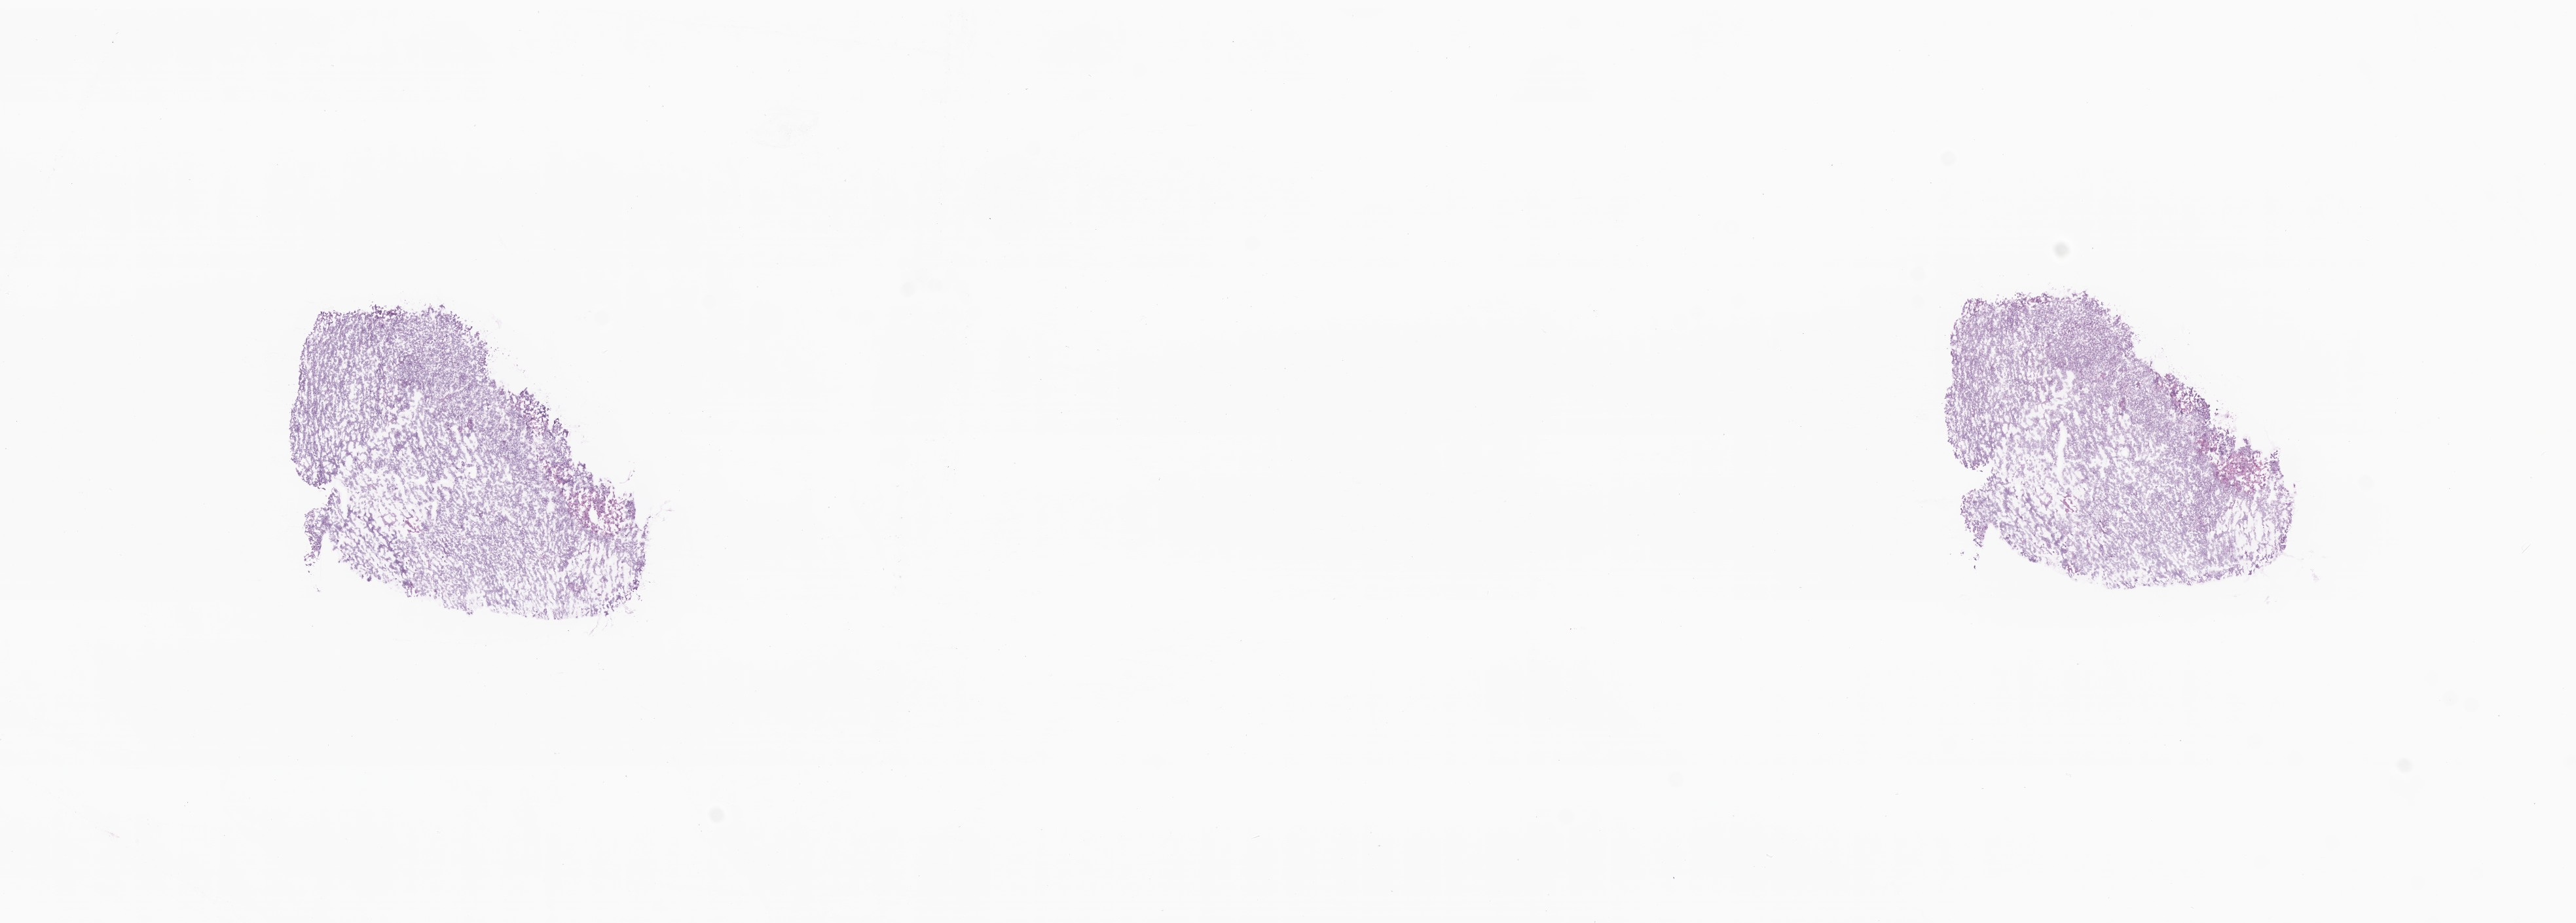
Digitized hematoxylin and eosin (H&E)-stained section, a low-resolution overview of the entire scanned area, about 16.6 x 5.9 mm, frozen section, primary tumor, anatomic site: body of uterus. Female patient. Tumor grade: G3 (poorly differentiated). Pathologist review of this section (percent, as recorded): tumor cells 80%, tumor nuclei 80%, stromal cells 20%, necrosis 0%, normal cells 0%. Inflammatory infiltration, as recorded: lymphocyte infiltration 0%, monocyte infiltration 0%, neutrophil infiltration 0%.
* AJCC pathologic stage: Stage IB
* histologic diagnosis: Carcinoma, undifferentiated, NOS